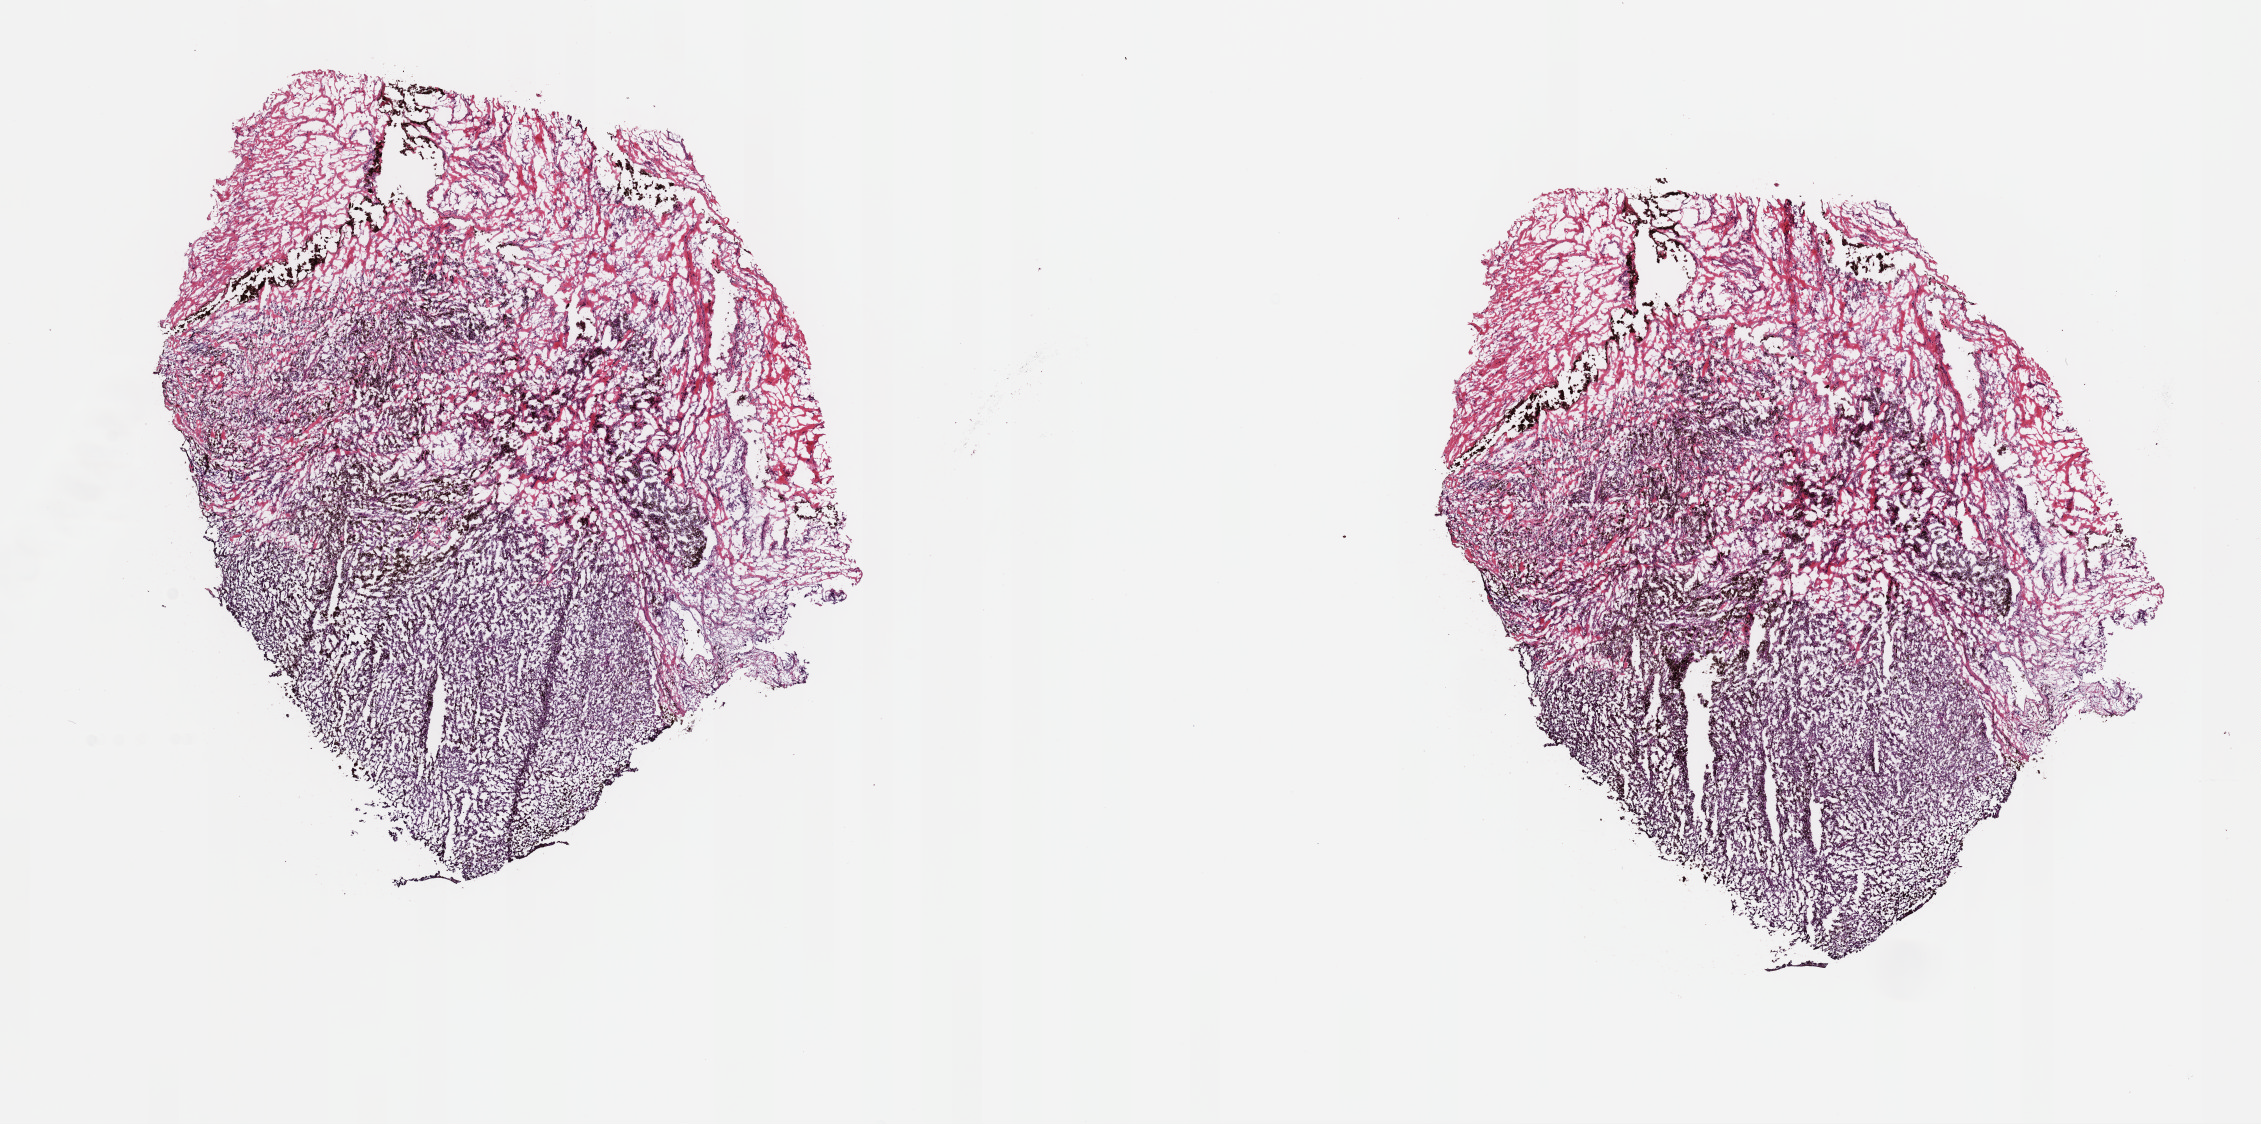
Digitized H&E tissue section (whole slide), low-resolution overview of the scanned area, about 17.9 x 8.9 mm. Frozen section from the top of the tissue portion. Metastatic tumour sample, sampled site: lymph nodes of head, face and neck. Male, age 63 years at initial diagnosis. Slide review estimates, as recorded: tumour cells 60%, tumour nuclei 75%, normal cells 40%, stromal cells 0%, necrosis 0%. Inflammatory infiltration, as recorded: lymphocyte infiltration 1%, monocyte infiltration 5%, neutrophil infiltration 0%.
• this section: metastatic tumour tissue
• patient diagnosis: Malignant melanoma, NOS